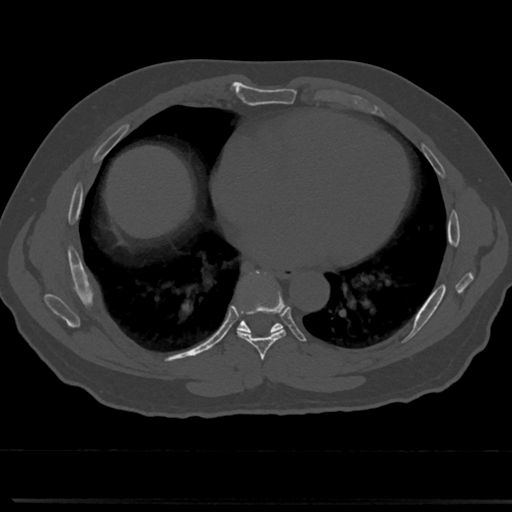
CT including the spine, one axial slice. Position 387 of 817 along the scan axis. Bone window (W 1800 / L 400 HU). 0.5 mm slice thickness. 512 × 512 image matrix, field of view 355 × 355 mm. Male patient, age 61 years. Case-level facts recorded for this patient, not image findings: primary cancer: prostate.
Annotated regions visible in this slice (semi-automatic segmentation, software-assisted and operator-edited):
- T6 vertebra: box from (x=260, y=364) to (x=269, y=377) px
- T7 vertebra: (x=221, y=274)–(x=309, y=355)